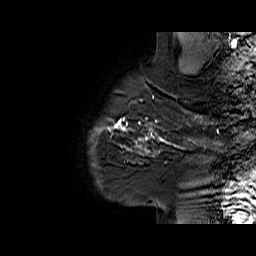
Breast MRI (dynamic contrast-enhanced), one sagittal slice. Slice 56 of 60 in the series (ordered by position). Dynamic contrast-enhanced series, time point 2 of 6 at this slice position (early post-contrast). 1.5 T. TE 6.1 ms, TR 32.9 ms. 4 mm slice thickness. 256 × 256 image matrix, field of view 220 × 220 mm. Female patient. Case-level facts recorded for this patient, not image findings: setting: breast cancer imaged before/during neoadjuvant chemotherapy; receptor status: HER2-positive.
Structures marked on this image (semi-automatic segmentation, software-assisted and operator-edited):
- analysis volume of interest (the breast-tissue region the enhancement analysis was run in; not a lesion): box from (x=127, y=95) to (x=194, y=165) px
- tumour enhancement mask (voxels above the 100 % enhancement threshold inside the analysis volume of interest): (x=127, y=96)–(x=181, y=154)